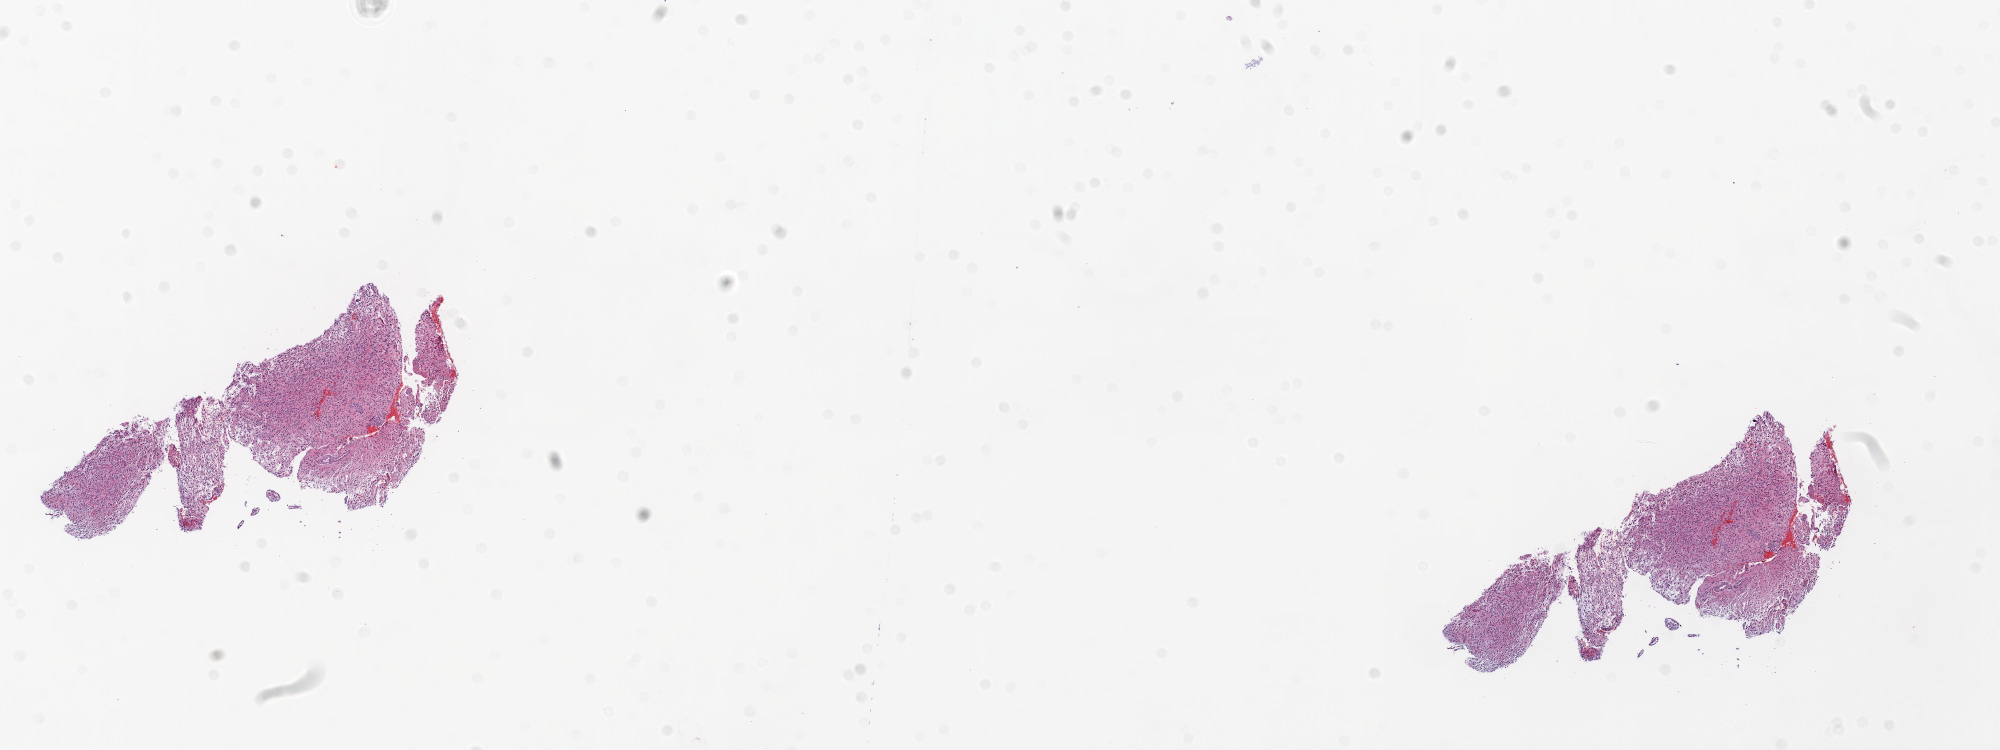
H&E whole-slide image — shown as a low-resolution overview of the whole scanned area (about 16.0 x 6.0 mm). Formalin-fixed paraffin-embedded (FFPE) diagnostic section. Brain, primary tumour sample. Female patient; age at initial diagnosis 72 years.
- diagnosis: Glioblastoma